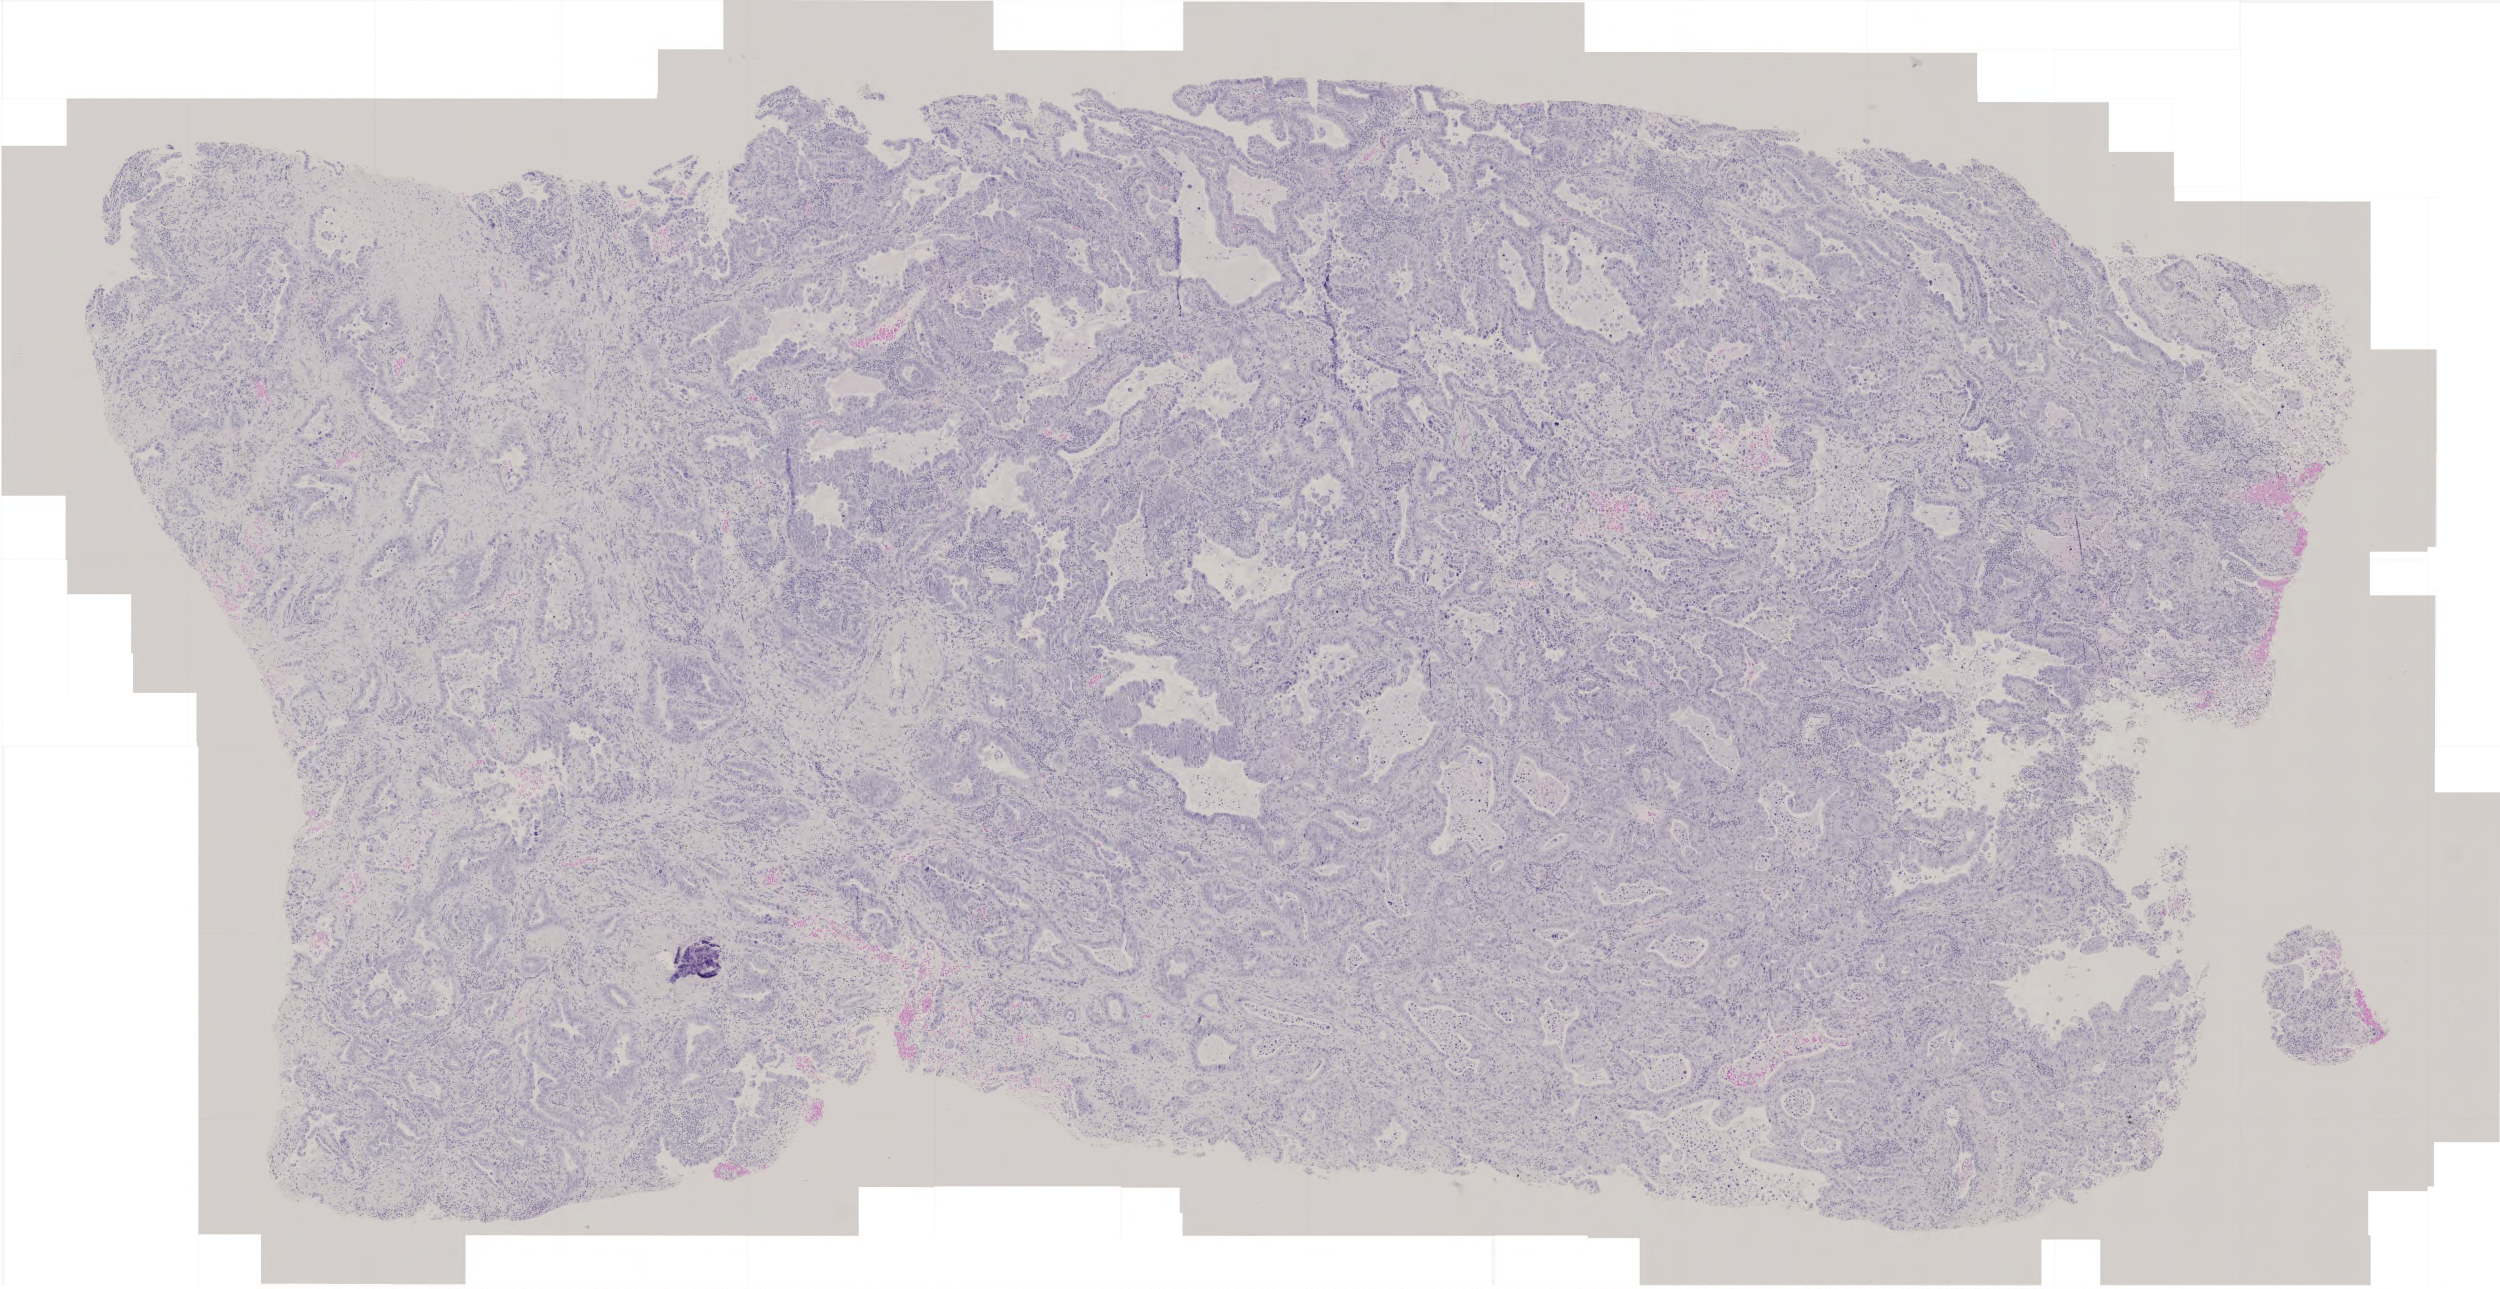
Digitized Hematoxylin and eosin (H&E) stained tissue section (whole slide) — whole scanned area (about 5.0 x 2.6 mm) shown as a low-resolution overview; formalin-fixed paraffin-embedded (FFPE) diagnostic section; primary tumour sample from the lung. Male, age 68 years at initial diagnosis.
Pathologic diagnosis: Adenocarcinoma with mixed subtypes.